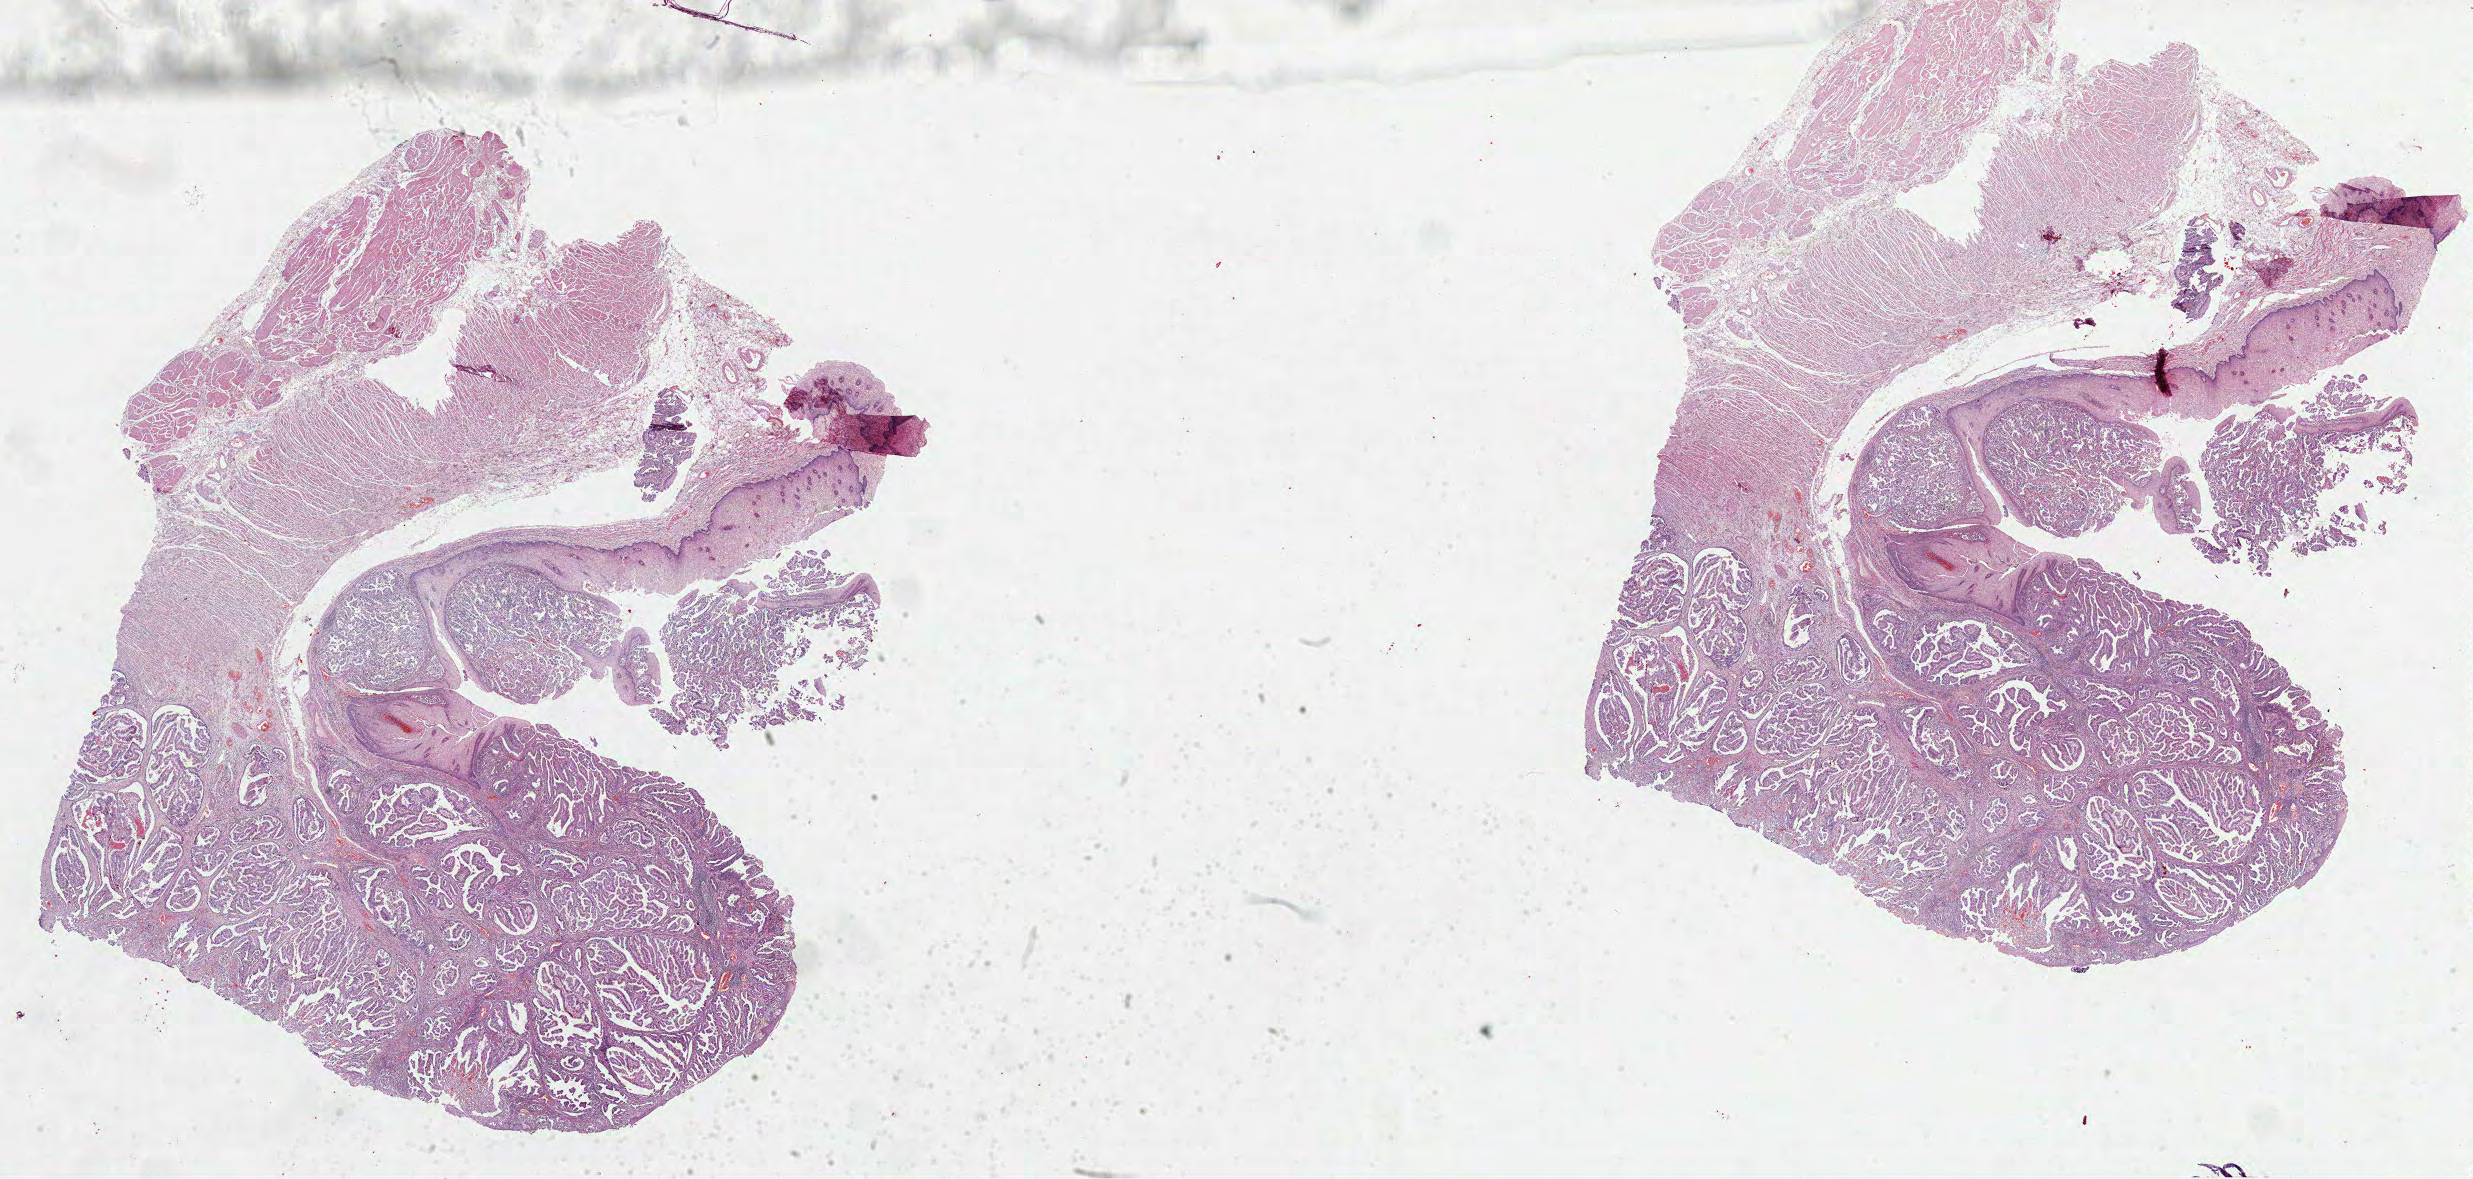
Whole-slide histology image, Hematoxylin and eosin (H&E) stained, shown as a low-resolution overview of the whole scanned area (about 39.9 x 19.0 mm, acquisition: 40x scan), formalin-fixed paraffin-embedded (FFPE) diagnostic section, stomach, primary tumour sample. Male patient; age at initial diagnosis 62 years. Histologic grade: G2 (moderately differentiated).
AJCC pathologic stage: II. TNM: T2 N1 M0. Histologic diagnosis: Papillary adenocarcinoma, NOS (cardia, NOS).